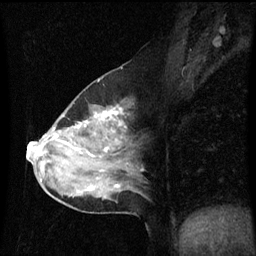
Breast MRI (dynamic contrast-enhanced), one sagittal slice; position 34 of 60 along the scan axis; dynamic contrast-enhanced series, image 2 of 3 at this slice position (ordered by acquisition); 1.5 T; TE 4.2 ms, TR 8.9 ms; 2 mm slice thickness; 256 × 256 image matrix, field of view 200 × 200 mm. Patient: female, 50 years. Case-level facts recorded for this patient, not image findings: setting: breast cancer imaged before/during neoadjuvant chemotherapy; receptor status: HR-positive, HER2-negative.
Structures marked on this image (semi-automatic segmentation, software-assisted and operator-edited):
- analysis volume of interest (the breast-tissue region the enhancement analysis was run in; not a lesion): bounding box [x1, y1, x2, y2] px = [33, 90, 139, 209]
- tumour enhancement mask (voxels above the 70 % enhancement threshold inside the analysis volume of interest): [33, 110, 119, 151]